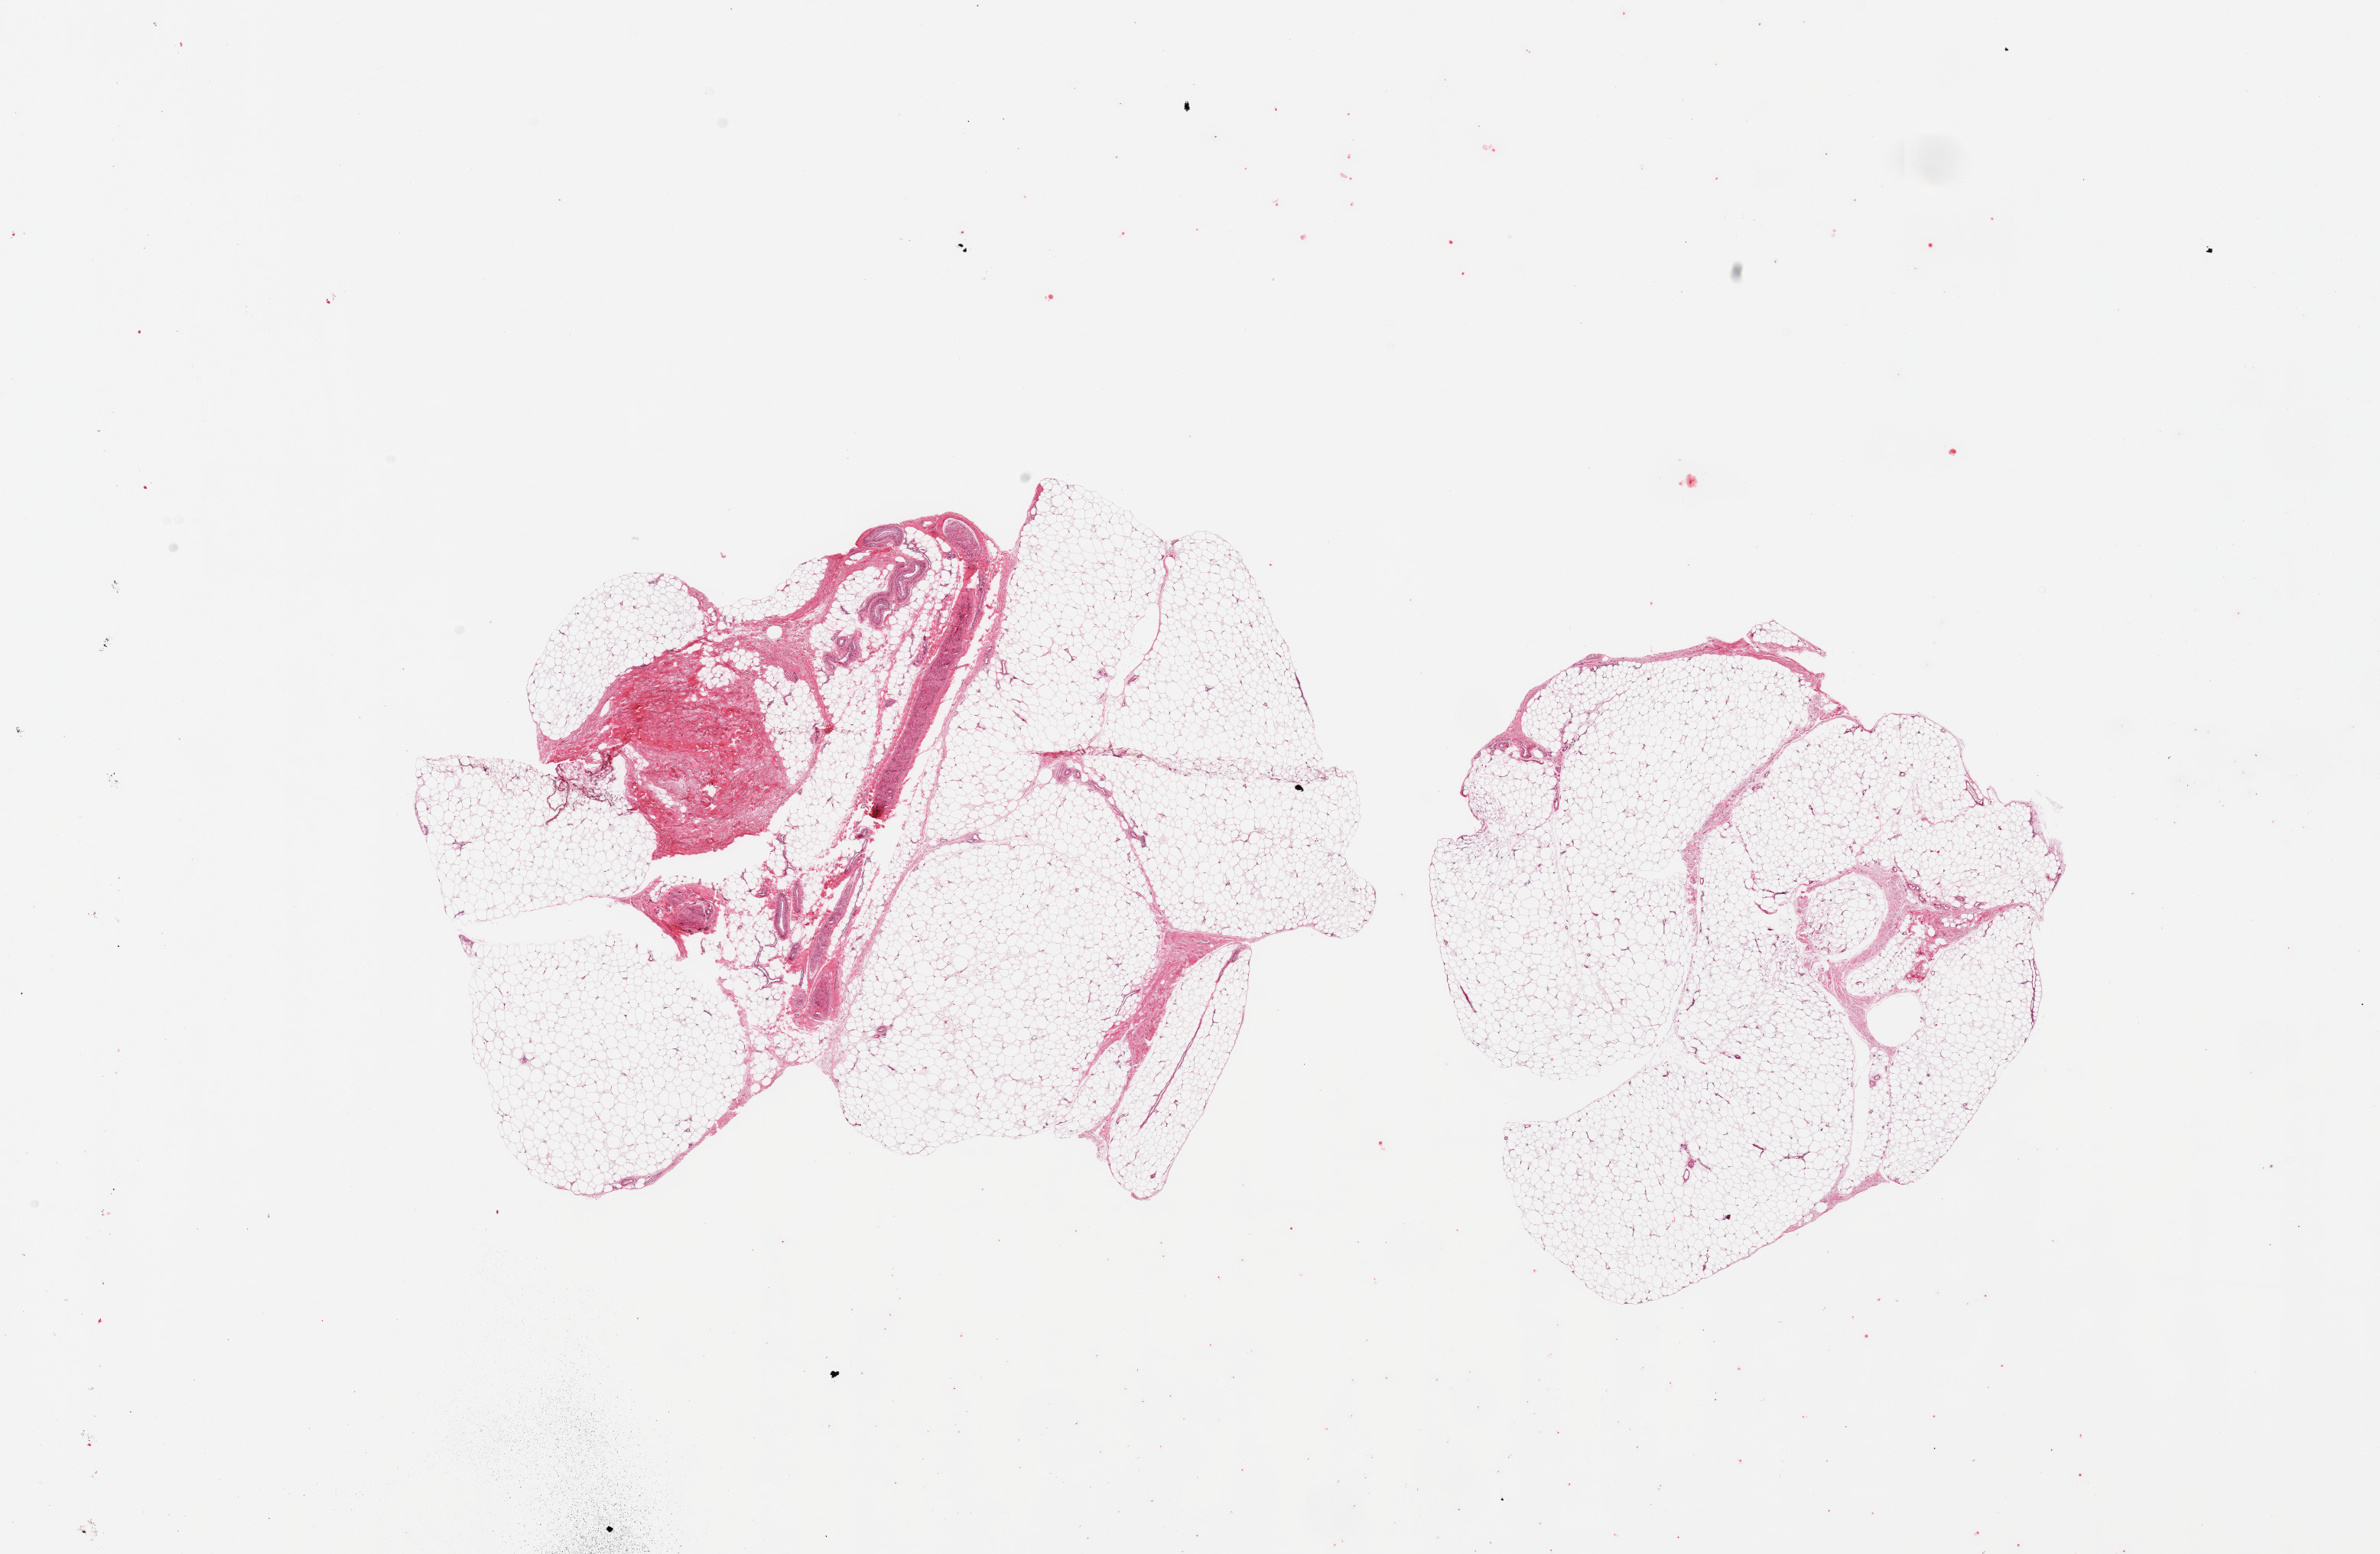
Whole-slide image, hematoxylin and eosin (H&E) stain — a low-resolution overview of the entire scanned area, about 24.6 x 16.1 mm (from a 20x scan); PAXgene-fixed, paraffin-embedded tissue; section of adipose tissue (target tissue); donor tissue sample. Male donor.
* review note (as recorded): 2 pieces: 1 is 98% fat, other contains 15% fibrovascular & neural tissue